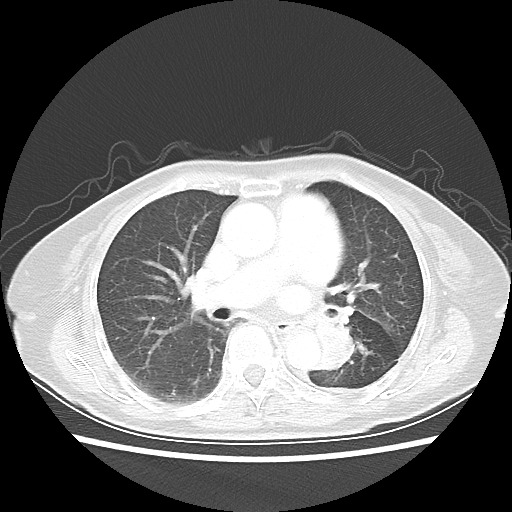
Chest CT, one axial slice; slice 27 of 50 in the series (ordered by position); lung window (W 1500 / L -600 HU); 5 mm slice thickness; 512 × 512 image matrix, field of view 335 × 335 mm. Patient: female, 81 years. From the clinical record (not read from this slice): clinical TNM (as recorded): T2 N0 M1a.
Outlined on this slice (rectangle marked by the reading radiologist):
- lung tumour (recorded histology: squamous cell carcinoma): bounding box (x1, y1, x2, y2) in pixels: (301, 302, 366, 386)